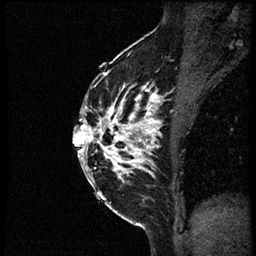
Breast MRI (dynamic contrast-enhanced), one sagittal slice. Dynamic contrast-enhanced study with each time point stored as its own series, time point 2 of 3 at this slice position (early post-contrast, ordered by acquisition time). 1.5 T. TE 4.2 ms, TR 21.3 ms. 256 × 256 image matrix, field of view 200 × 200 mm. Patient: female, 41 years. From the clinical record (not read from this slice): setting: breast cancer imaged before/during neoadjuvant chemotherapy; receptor status: HER2-positive.
Structures marked on this image (semi-automatic segmentation, software-assisted and operator-edited):
- analysis volume of interest (the breast-tissue region the enhancement analysis was run in; not a lesion): bounding box <84,73,177,205> (left, top, right, bottom; pixels)
- tumour enhancement mask (voxels above the 100 % enhancement threshold inside the analysis volume of interest): <84,73,164,183>